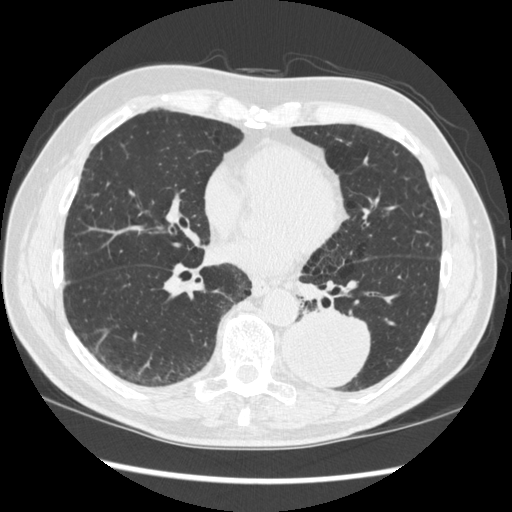
Axial slice from a low-dose chest CT screening exam; first (baseline) screen; lung window (W 1500 / L -600 HU); standard (soft-tissue) reconstruction kernel (STANDARD); slice 142 of 348 in the series. Male participant, aged 72 years at enrolment. Current smoker at enrolment.
Expert reader's lesion annotation, bounding box (x1, y1, x2, y2) in pixels: (269, 301, 373, 392). The screening reader recorded 2 non-calcified nodules or masses ≥4 mm on this exam (left lower lobe, right middle lobe); which of them this box marks is not recorded. Official screen result: positive, change unspecified: nodule(s) >= 4 mm or enlarging nodule(s), mass(es), or other non-specific abnormalities suspicious for lung cancer. Lung cancer was diagnosed 37 days after this screen: squamous cell carcinoma, NOS, left lower lobe, stage IIIA (AJCC 6th edition), 60 mm at pathology.